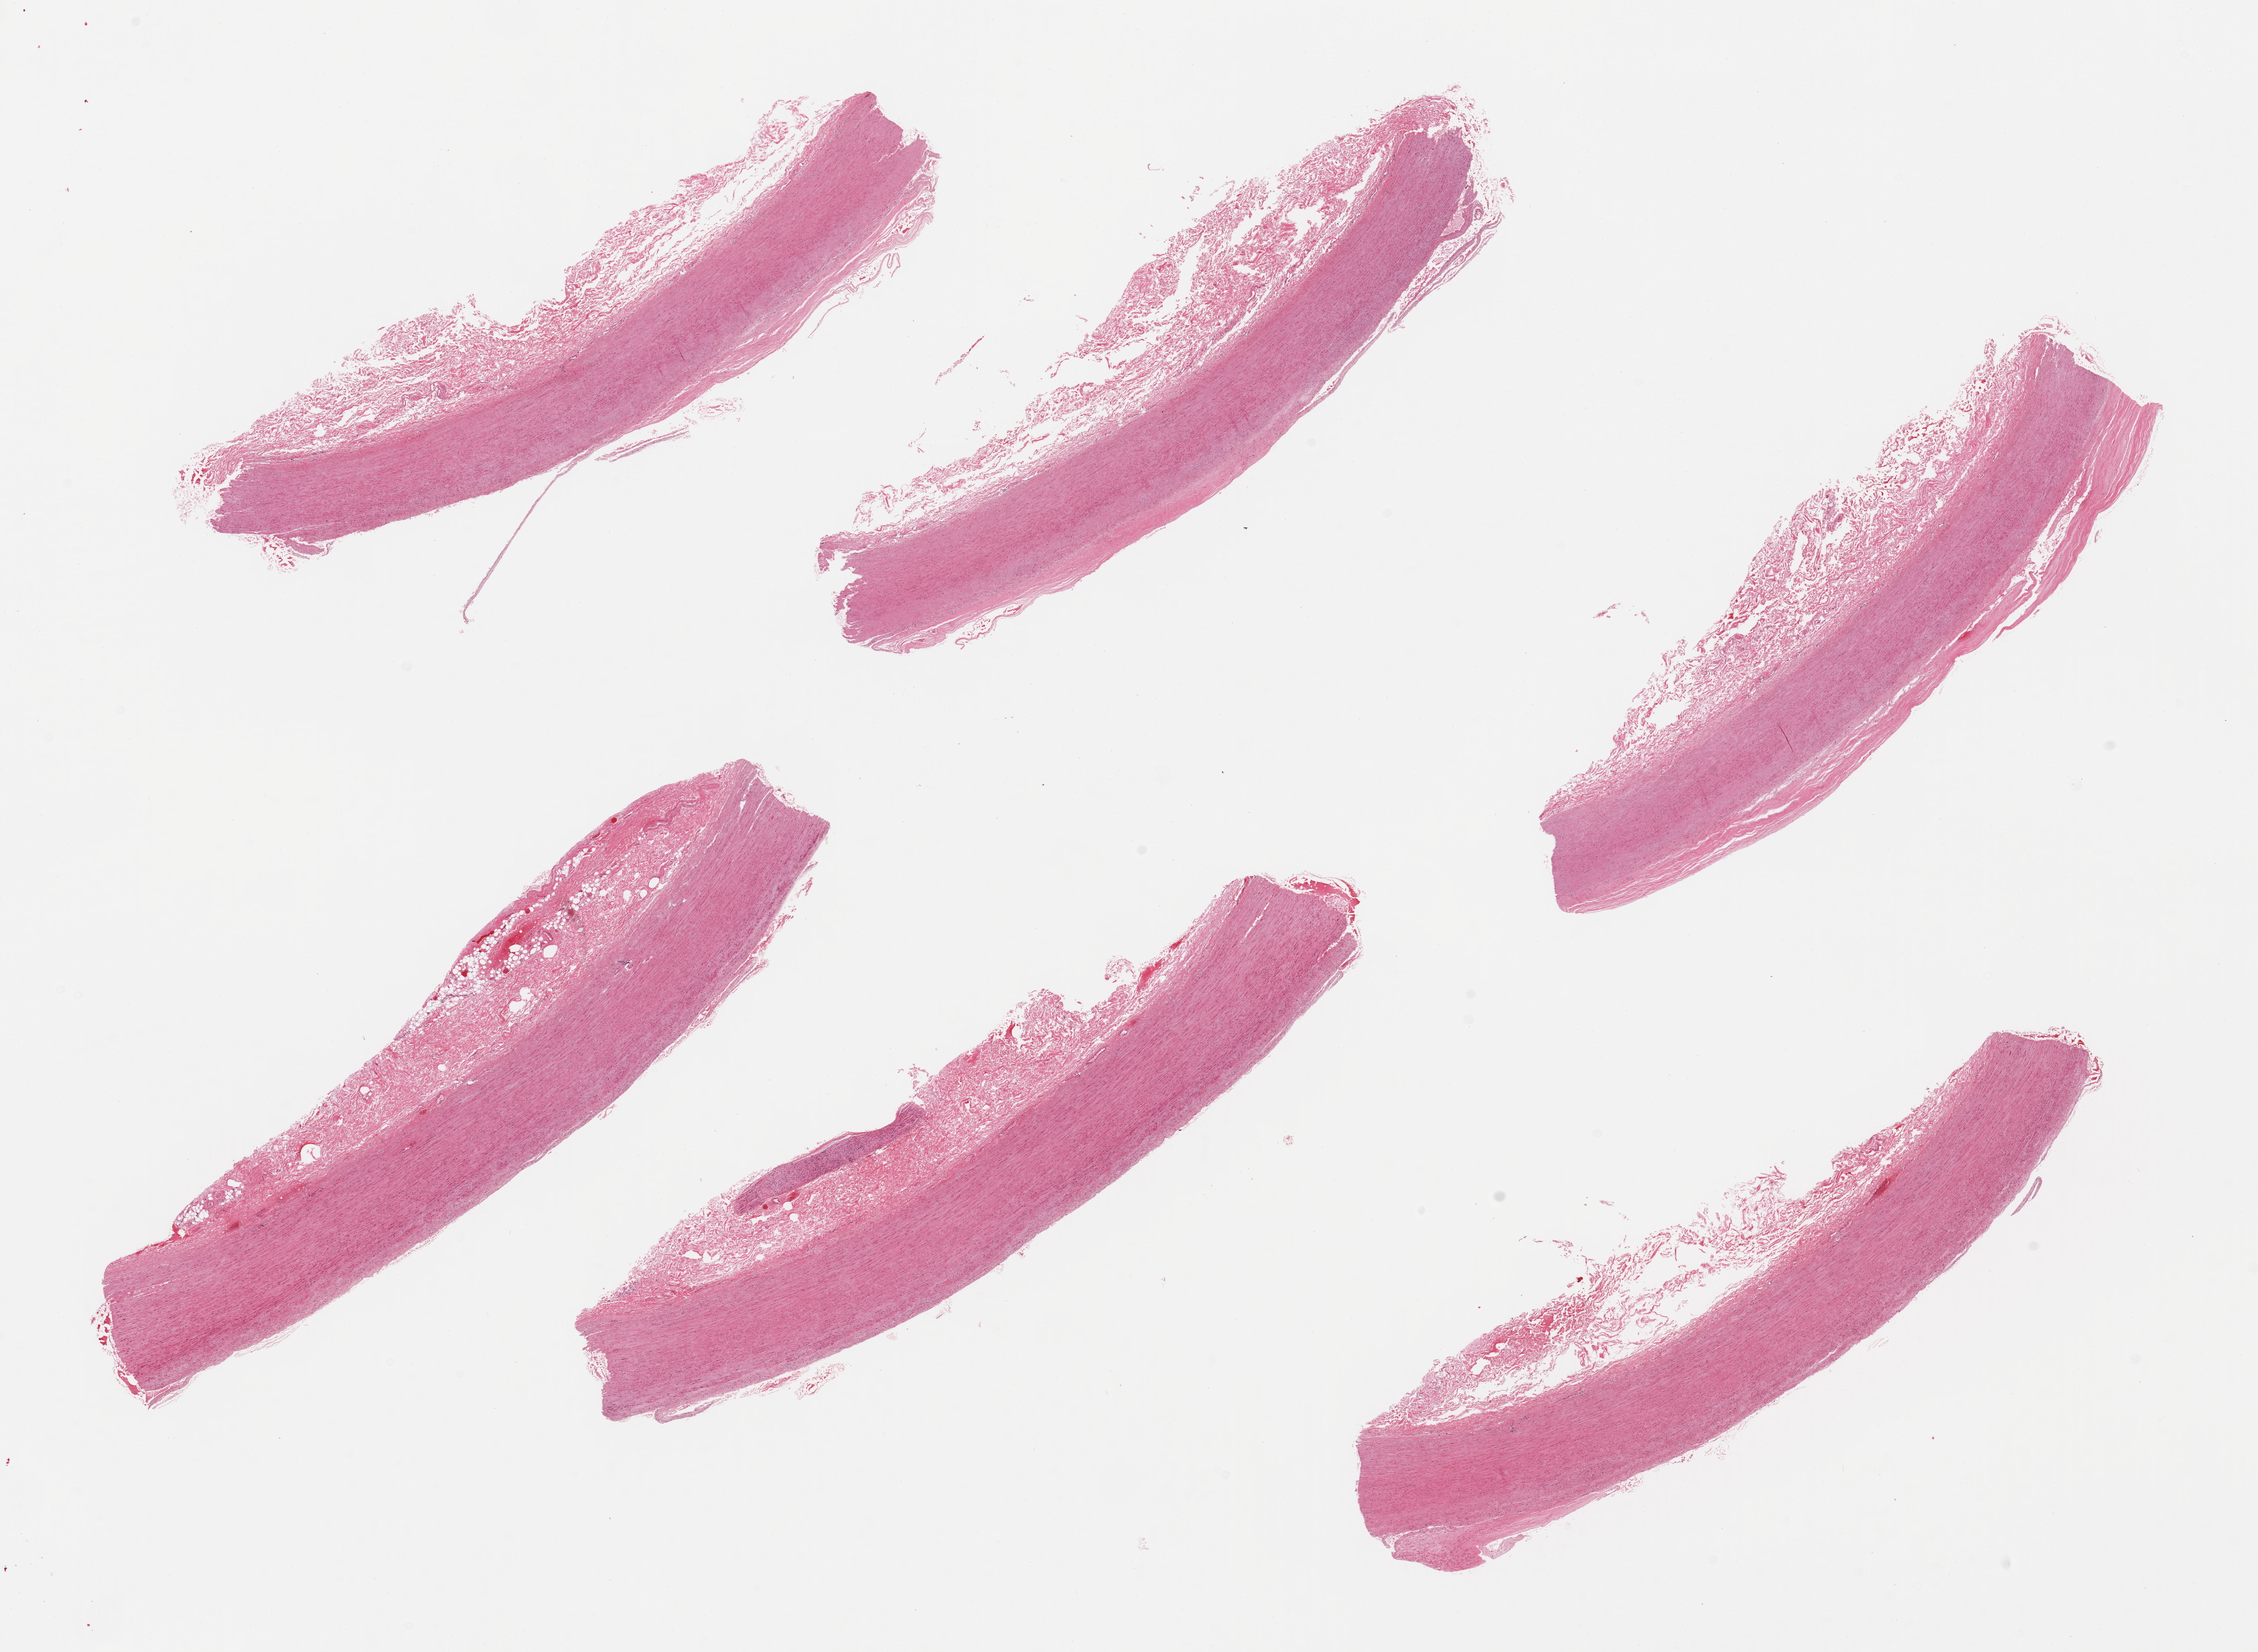
Hematoxylin and eosin (H&E) whole-slide image — whole scanned area (about 26.6 x 19.4 mm, acquisition: 20x scan) shown as a low-resolution overview. PAXgene-fixed, paraffin-embedded tissue. Section of aorta (target tissue). Donor tissue sample. Male donor.
* review note (as recorded): 6 pieces; attached adventitia and nerve; atherosclerosis